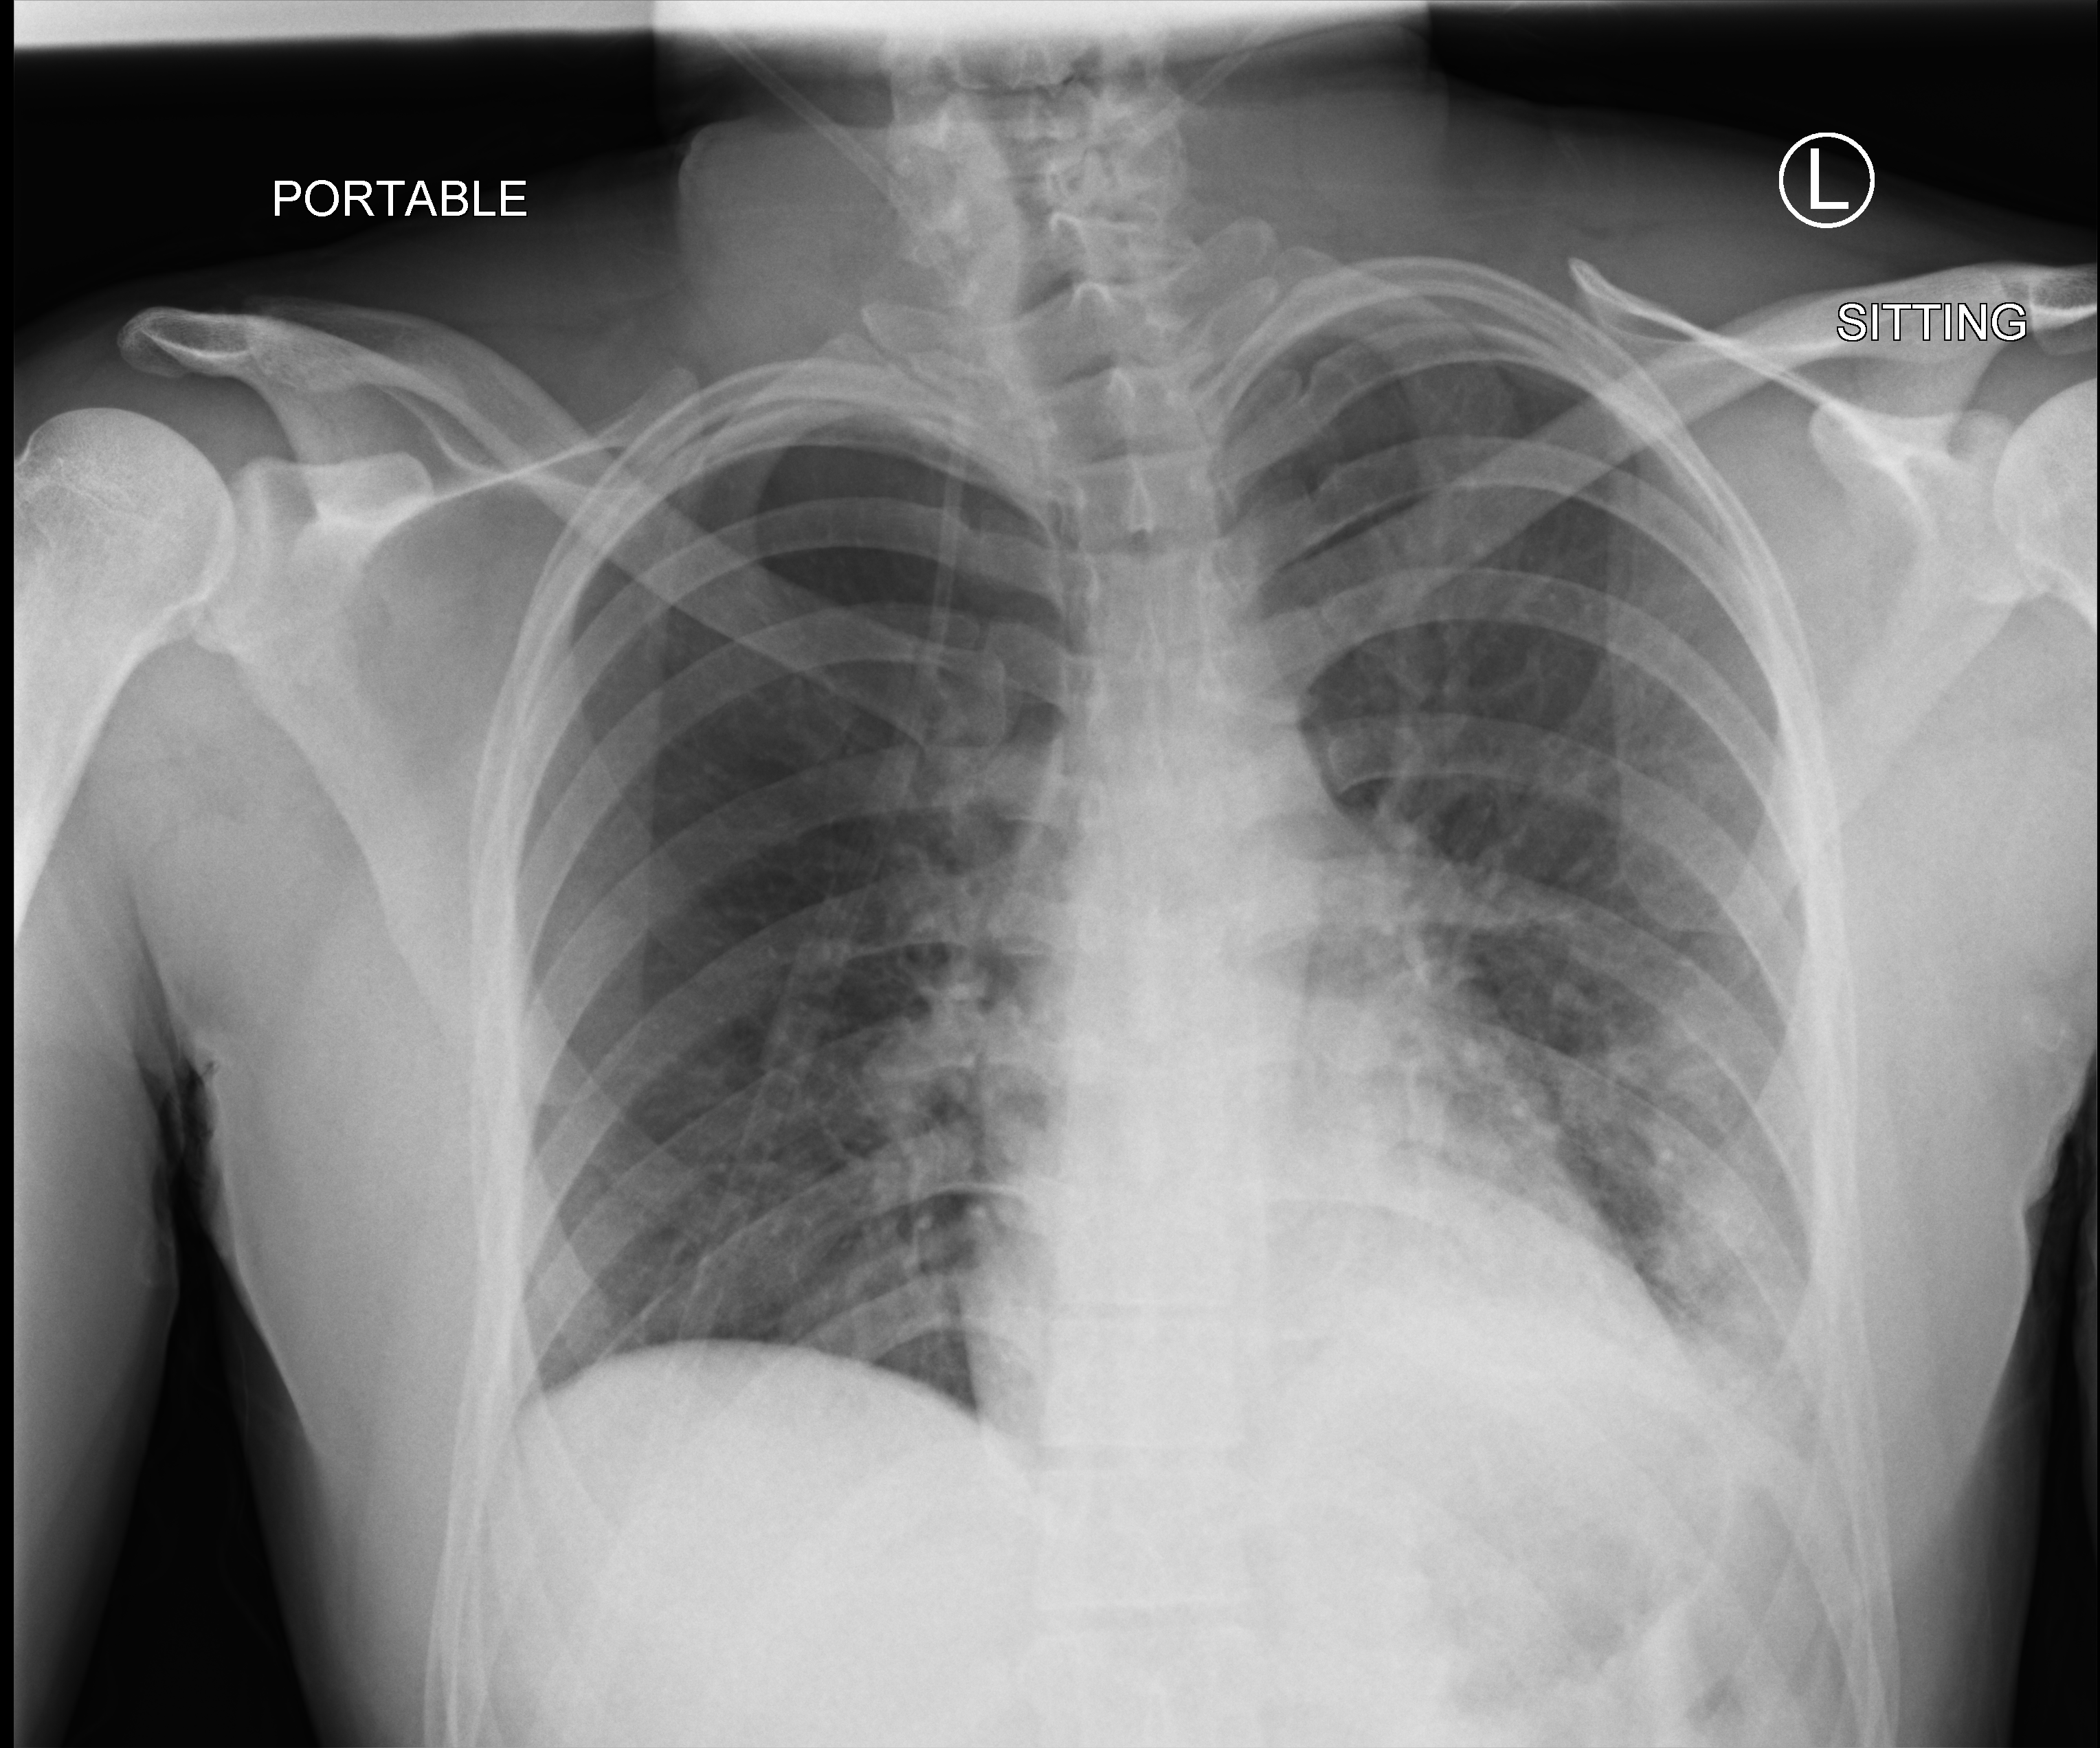
Portable chest radiograph, anteroposterior (AP) projection. Male patient hospitalised with COVID-19, age 18–59 years.
From the hospital-stay record, not from the radiograph (when in the stay this image was taken is not recorded):
- admitted to intensive care during this hospital stay: no